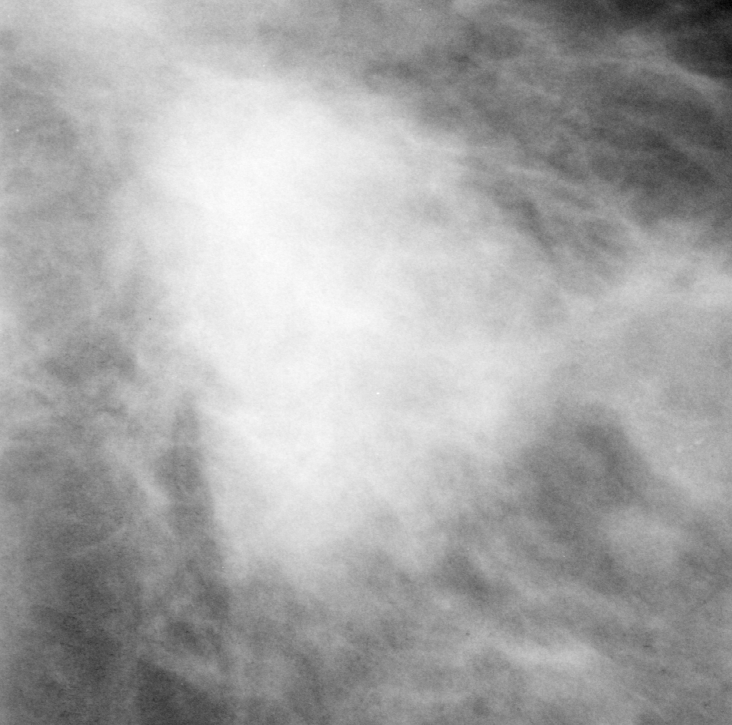
Crop from a digitized film mammogram around one marked abnormality, left breast, CC view.
Mass, shape irregular, margins ill defined; BI-RADS assessment category 5; subtlety rating 5 on a 1 (subtle) to 5 (obvious) scale; pathology (as recorded): malignant.